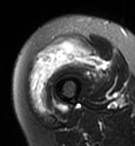
MRI of an extremity soft-tissue mass, one axial slice; position 24 of 95 along the scan axis; T2-weighted fat-saturated; MR volume resampled by the dataset authors to the PET/CT grid (not the native acquisition matrix); 135 × 146 image matrix. Female patient. From the clinical record (not read from this slice): histological type: pleiomorphic undifferentiated sarcoma; grade: high; site of the primary tumour: right quadricep.
Outlined on this slice (expert contour drawn on MRI and transferred to this co-registered scan by the dataset authors):
- gross tumour volume including surrounding oedema: bounding box <30,36,100,110> (left, top, right, bottom; pixels)